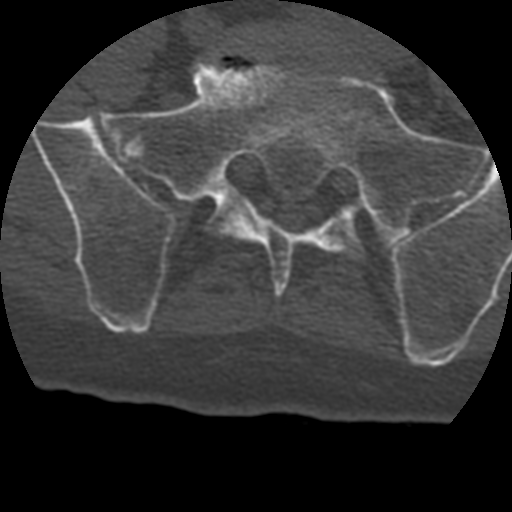
CT including the spine, one axial slice; position 23 of 399 along the scan axis; bone window (W 1800 / L 400 HU); 1.25 mm slice thickness; 512 × 512 image matrix. Patient age 69 years. Case-level facts recorded for this patient, not image findings: primary cancer: prostate.
Annotated regions visible in this slice (semi-automatic segmentation, software-assisted and operator-edited):
- L5 vertebra: bounding box (x1, y1, x2, y2) in pixels: (247, 27, 252, 32)